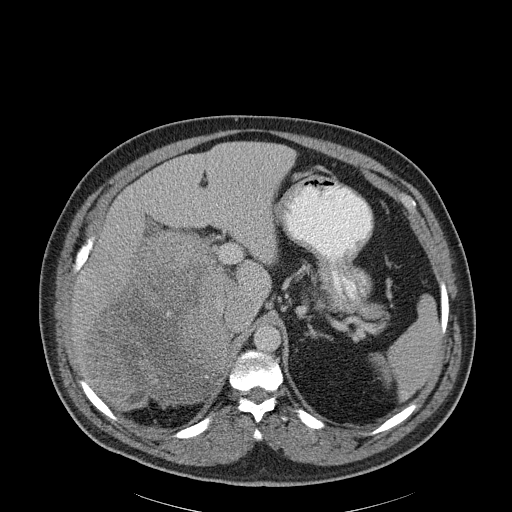
Contrast-enhanced abdominal CT, one axial slice. Slice 140 of 186 in the series (ordered by position). Reconstruction kernel B30f. Soft-tissue window (W 400 / L 40 HU). 3 mm slice thickness. 512 × 512 image matrix. Male patient, age 56 years. From the clinical record (not read from this slice): diagnosis: adrenocortical carcinoma; tumour side: right adrenal; tumour size at pathology: 18 cm; Ki-67 index: 2 %; stage (as recorded): 3.
Annotated regions visible in this slice (semi-automatic segmentation, software-assisted and operator-edited):
- mass: bounding box (x1, y1, x2, y2) in pixels: (85, 235, 224, 402)